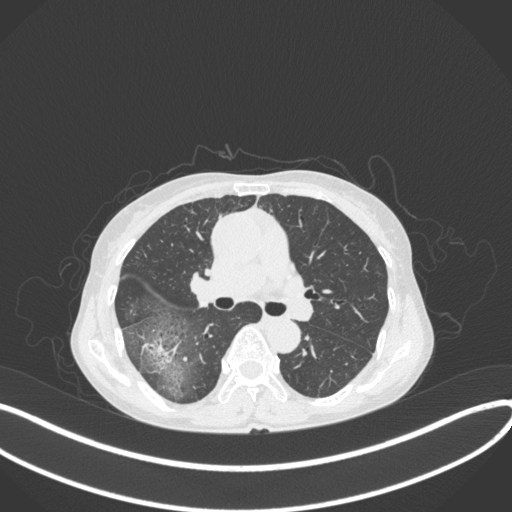
Chest CT, one axial slice; position 236 of 379 along the scan axis; reconstruction kernel B31f; 120 kVp; lung window (W 1500 / L -600 HU); 1 mm slice thickness; 512 × 512 image matrix. Female patient, age 69 years. From the clinical record (not read from this slice): clinical TNM (as recorded): T1b N0 M0; histopathological grade: G2-3.
Annotated regions visible in this slice (bounding box drawn by a radiologist):
- lung tumour (recorded histology: adenocarcinoma): box from (x=143, y=333) to (x=180, y=372) px